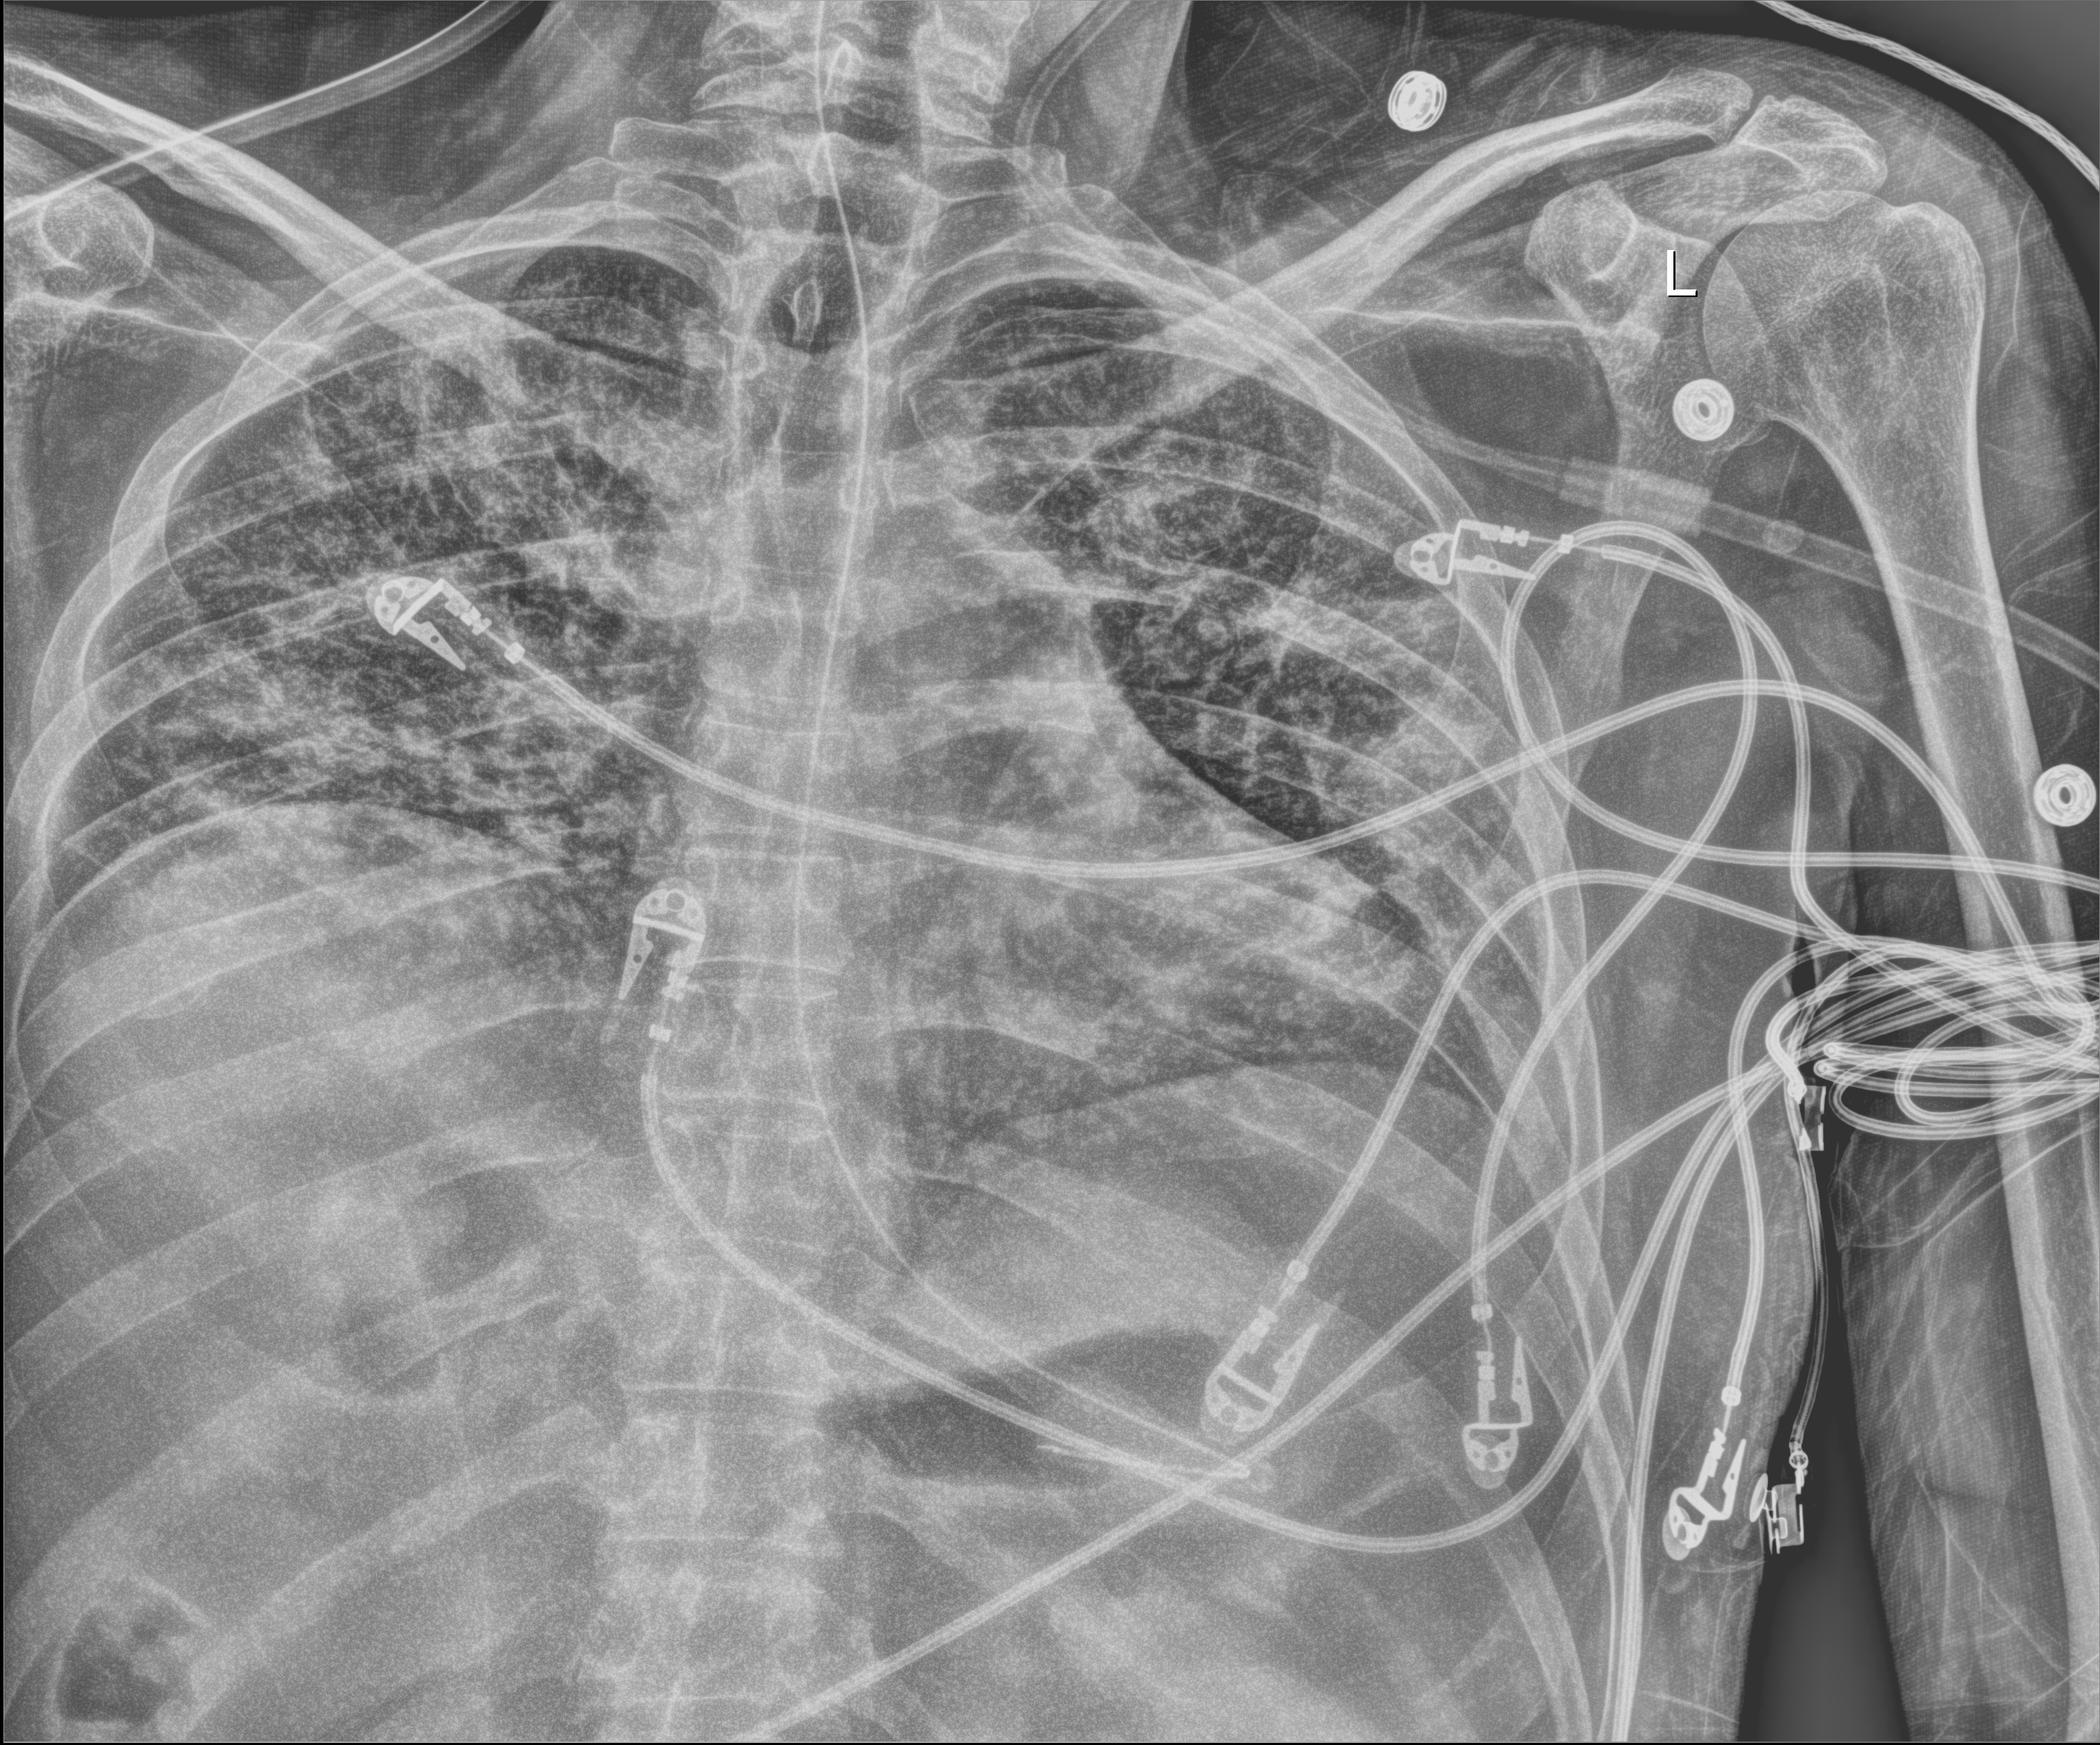
Bedside chest radiograph (digital radiography), anteroposterior (AP) projection. Patient hospitalised with COVID-19; male, aged 18–59 years.
Hospital-stay facts (about this admission, not read from this image; timing relative to this image not recorded): admitted to intensive care during this hospital stay: yes.